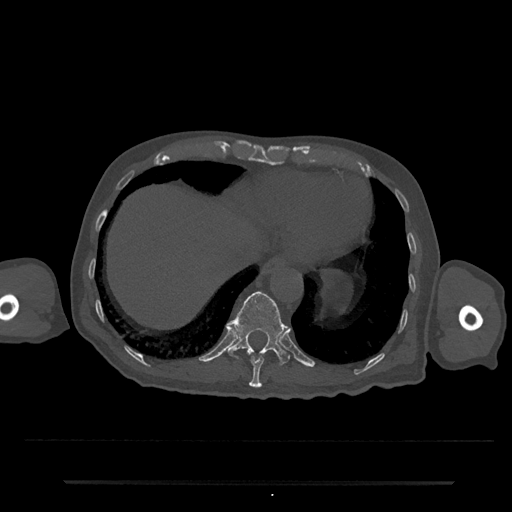
CT including the spine, one axial slice. Slice 275 of 797 in the series (ordered by position). Bone window (W 1800 / L 400 HU). 0.5 mm slice thickness. 512 × 512 image matrix, field of view 427 × 427 mm. Patient: male, 74 years. From the clinical record (not read from this slice): primary cancer: prostate.
Annotated regions visible in this slice (semi-automatic segmentation, software-assisted and operator-edited):
- T10 vertebra: bounding box (x1, y1, x2, y2) in pixels: (249, 355, 264, 388)
- T11 vertebra: (228, 291, 290, 365)